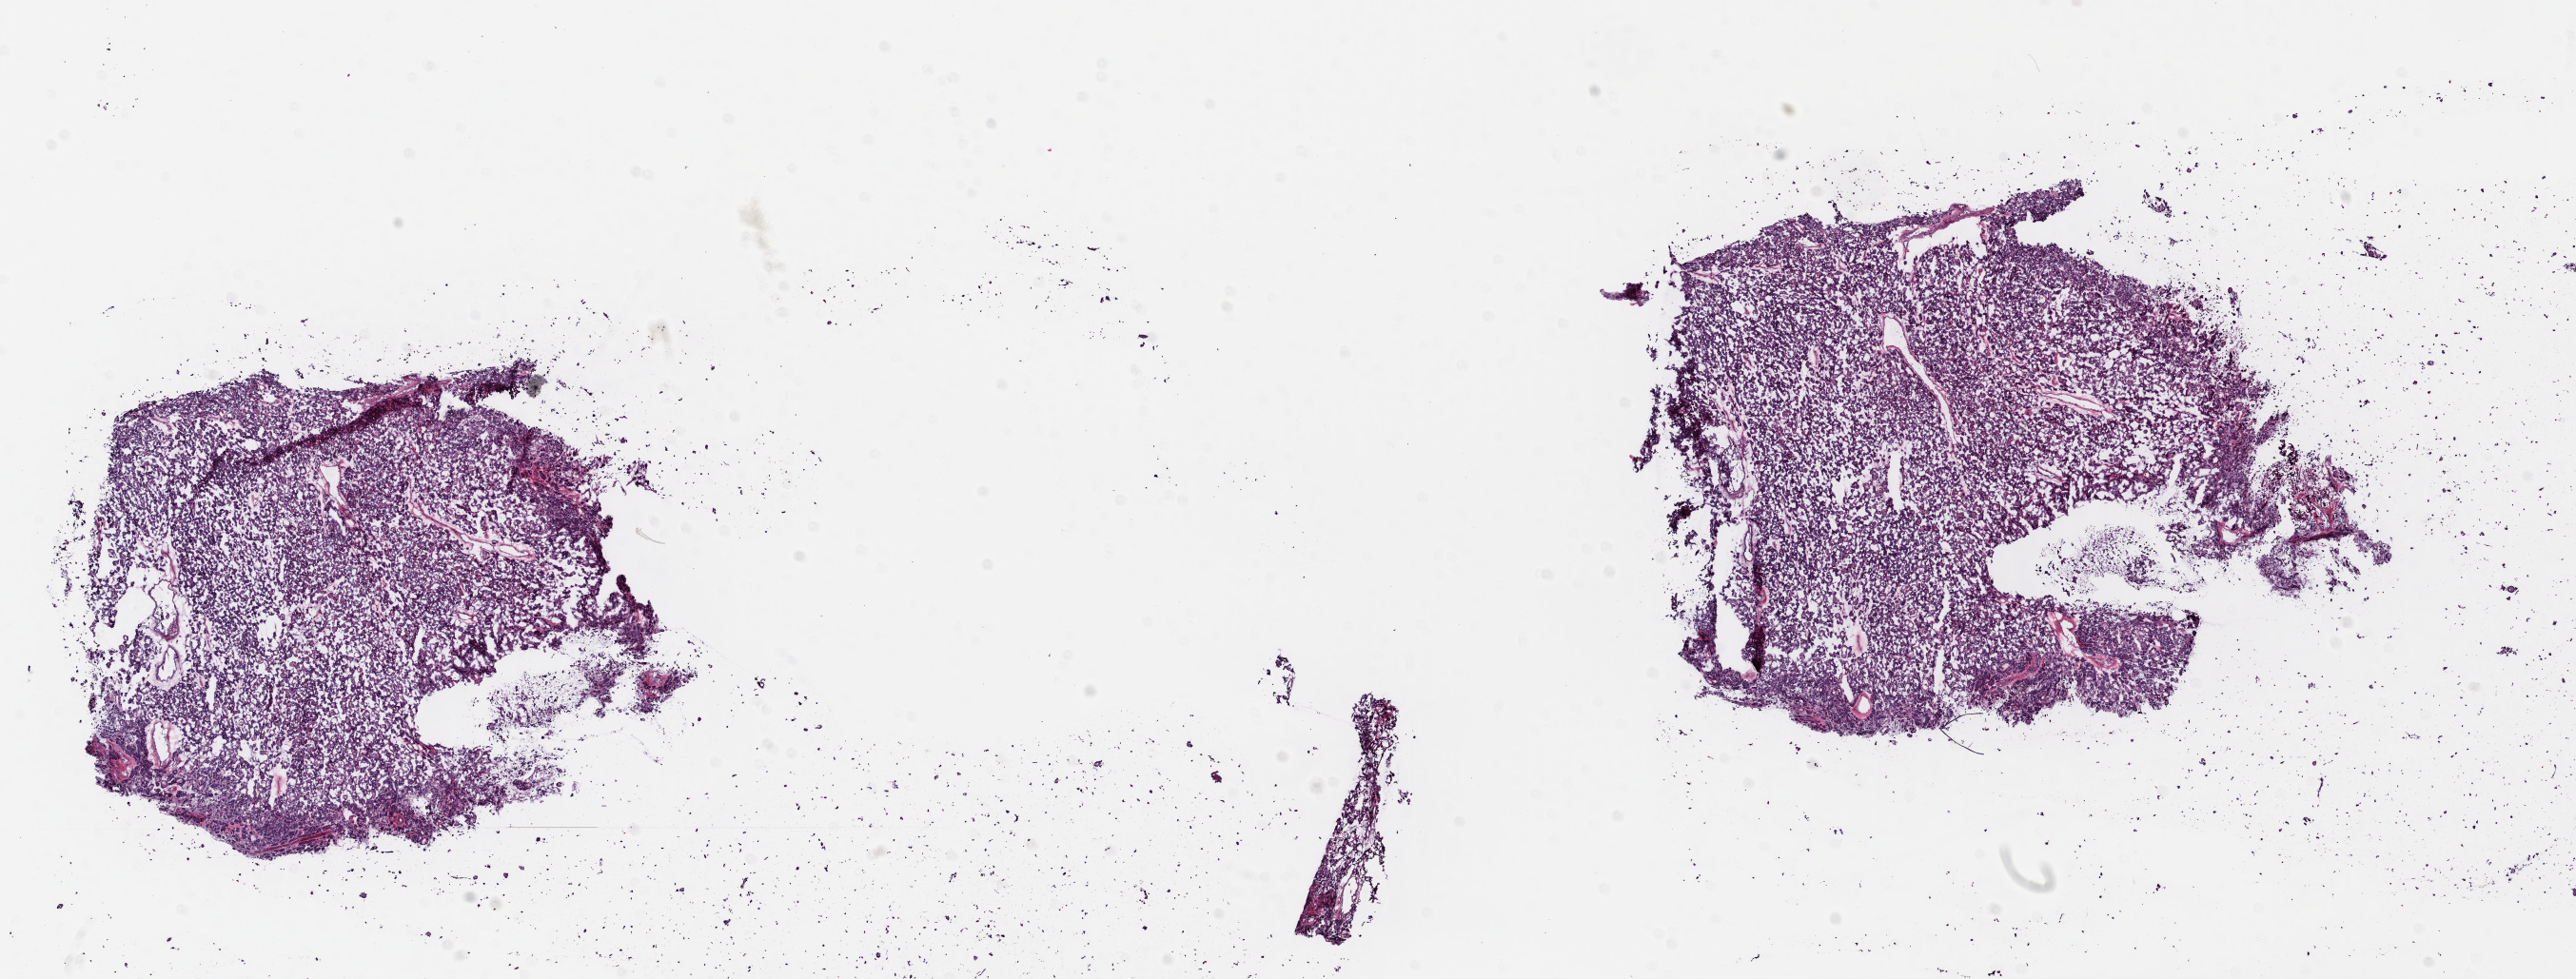
Digitized H&E-stained tissue section (whole slide) — whole scanned area (about 21.3 x 8.1 mm) shown as a low-resolution overview, frozen section from the top of the tissue portion, thyroid, primary tumour sample. Female, age 71 years at initial diagnosis. Composition of this section per pathologist review: tumour cells 90%, tumour nuclei 96%, normal cells 5%, stromal cells 5%, necrosis 0%. Inflammatory infiltration, as recorded: lymphocyte infiltration 1%, monocyte infiltration 0%, neutrophil infiltration 0%.
* pathologic diagnosis: Papillary carcinoma, follicular variant (thyroid gland)
* lymph nodes positive (case pathology): 0 of 1 examined
* AJCC pathologic stage: III (6th edition)